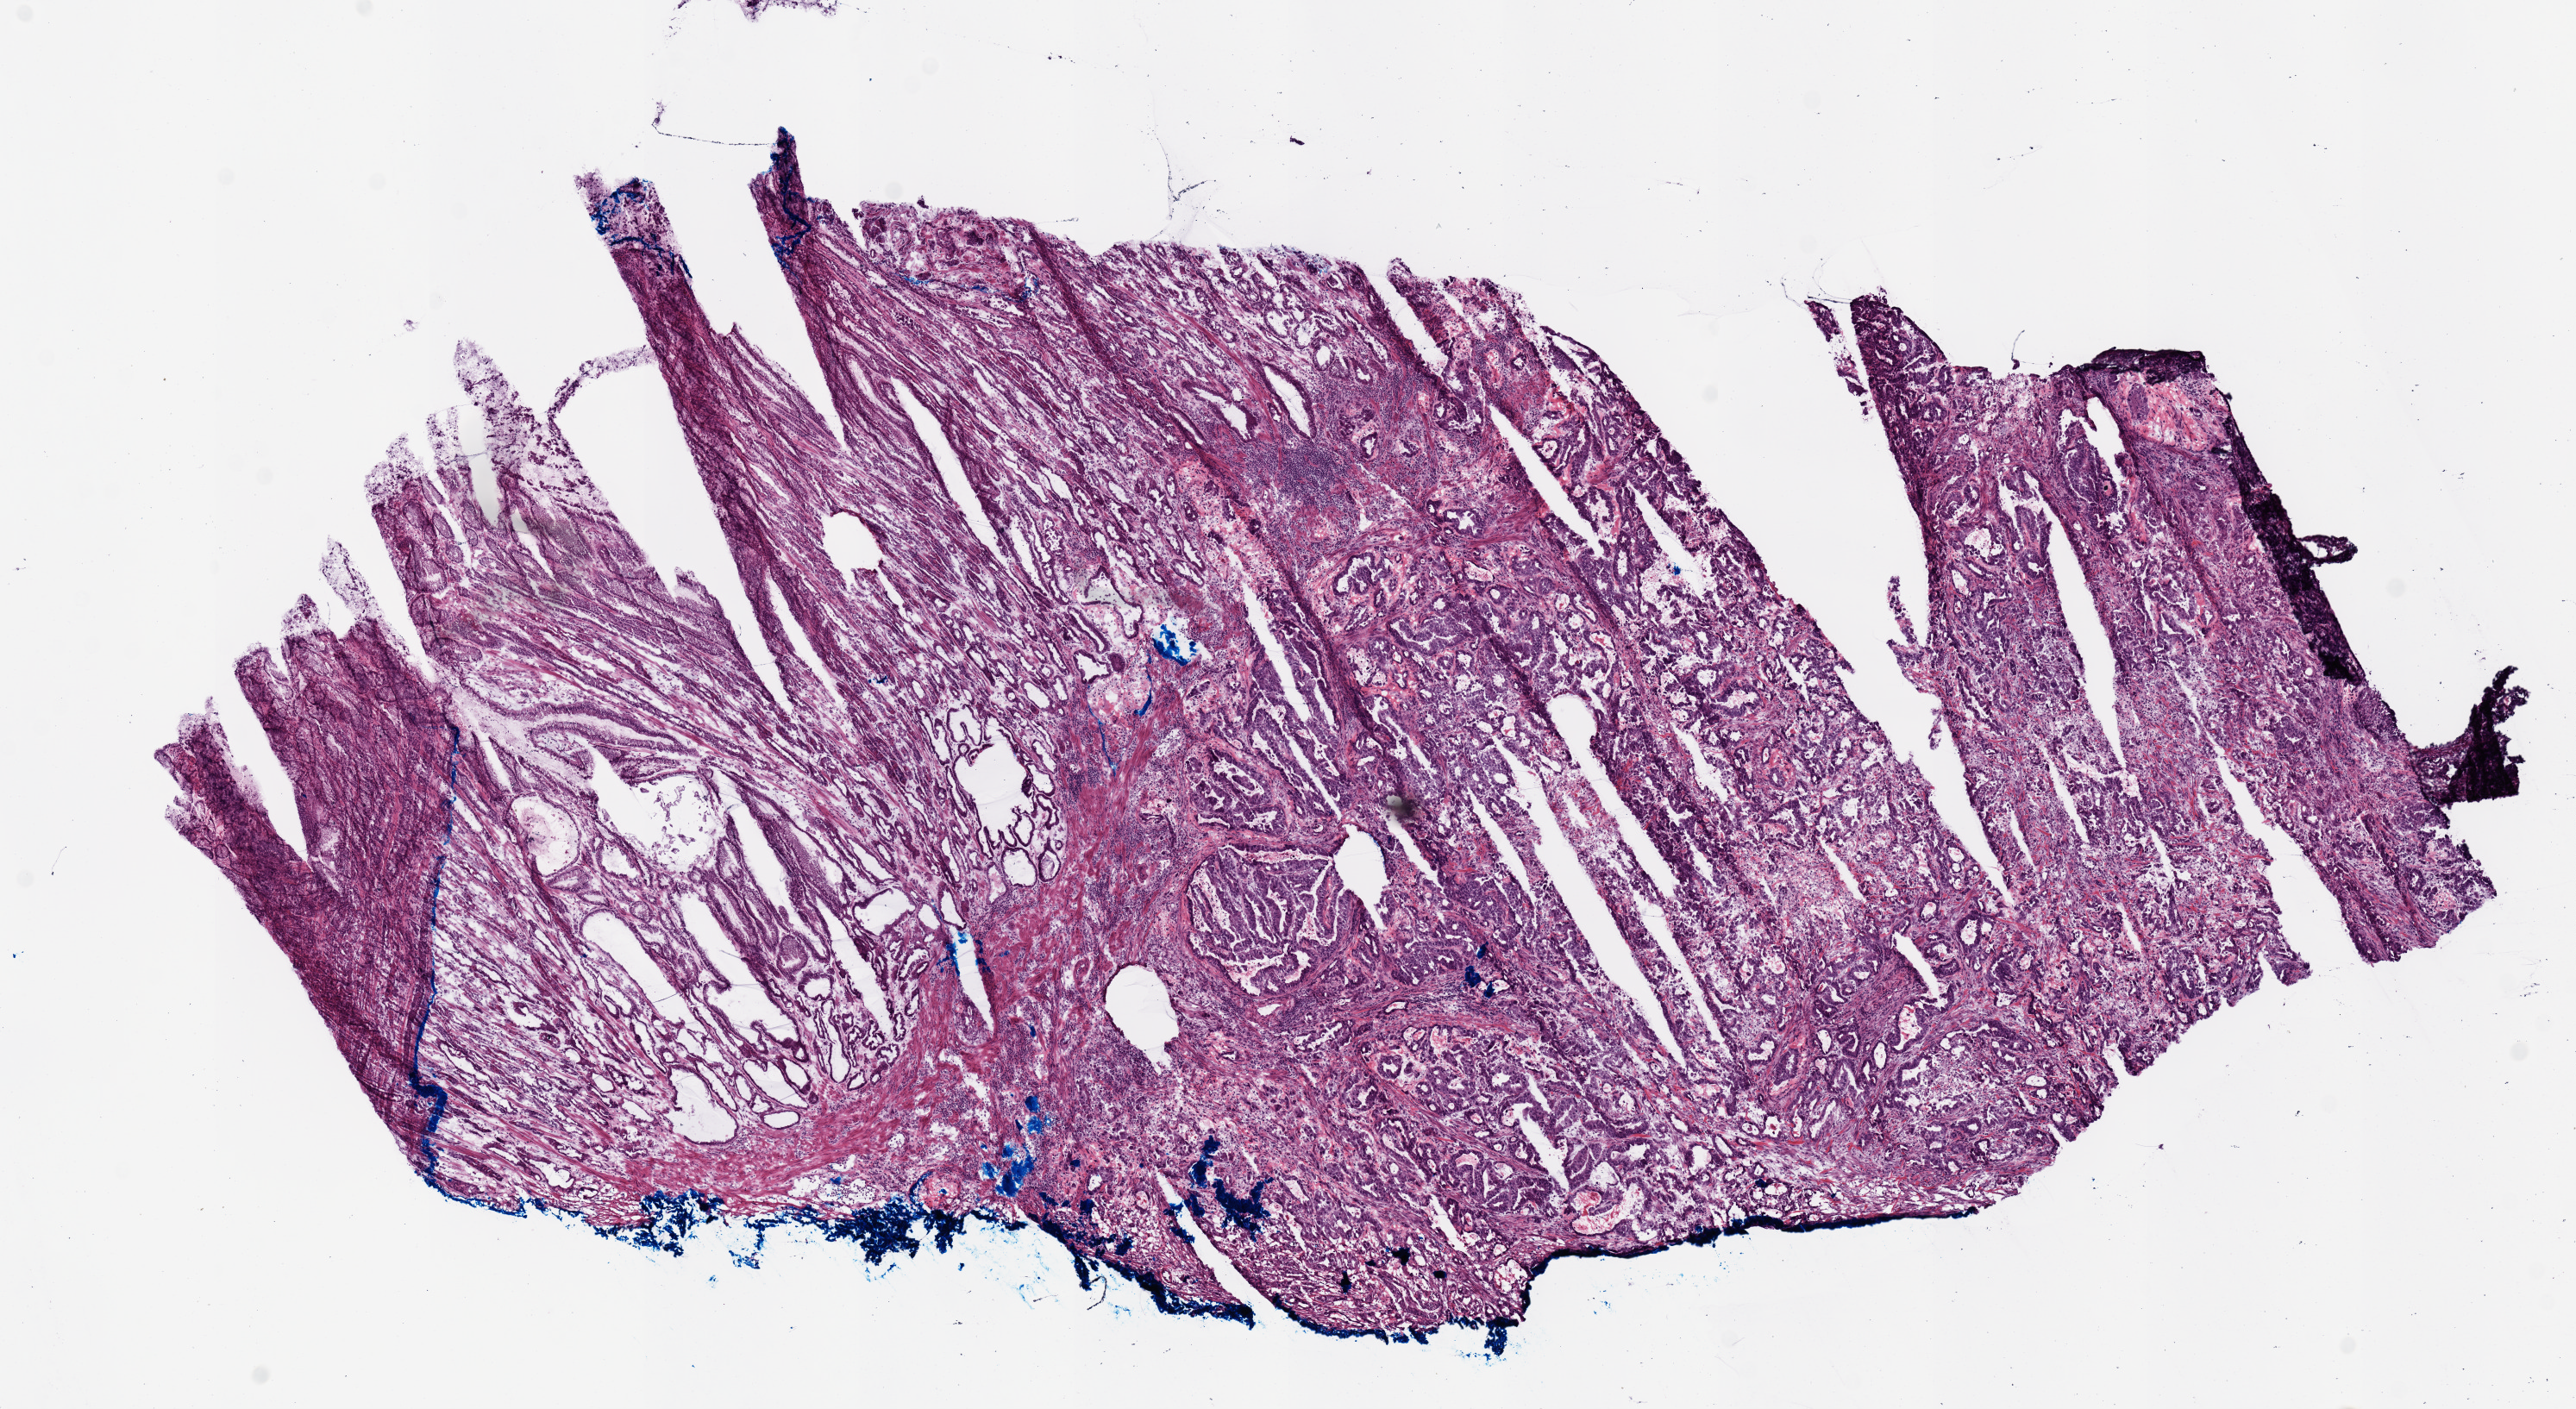
Hematoxylin and eosin (H&E) stained whole-slide image, a low-resolution overview of the entire scanned area, about 11.8 x 6.5 mm. Frozen section from the top of the tissue portion. Stomach, primary tumour sample. Male, age 68 years at initial diagnosis. Histologic grade: G2 (moderately differentiated). Slide review estimates, as recorded: tumour cells 100%, tumour nuclei 70%, normal cells 0%, stromal cells 0%, necrosis 0%. Inflammatory infiltration, as recorded: lymphocyte infiltration 15%, monocyte infiltration 0%, neutrophil infiltration 5%.
* lymph nodes positive (case pathology): 6 of 25 examined
* diagnosis: Adenocarcinoma, intestinal type (cardia, NOS)
* AJCC pathologic stage: IIIA
* TNM: T3 N2 MX